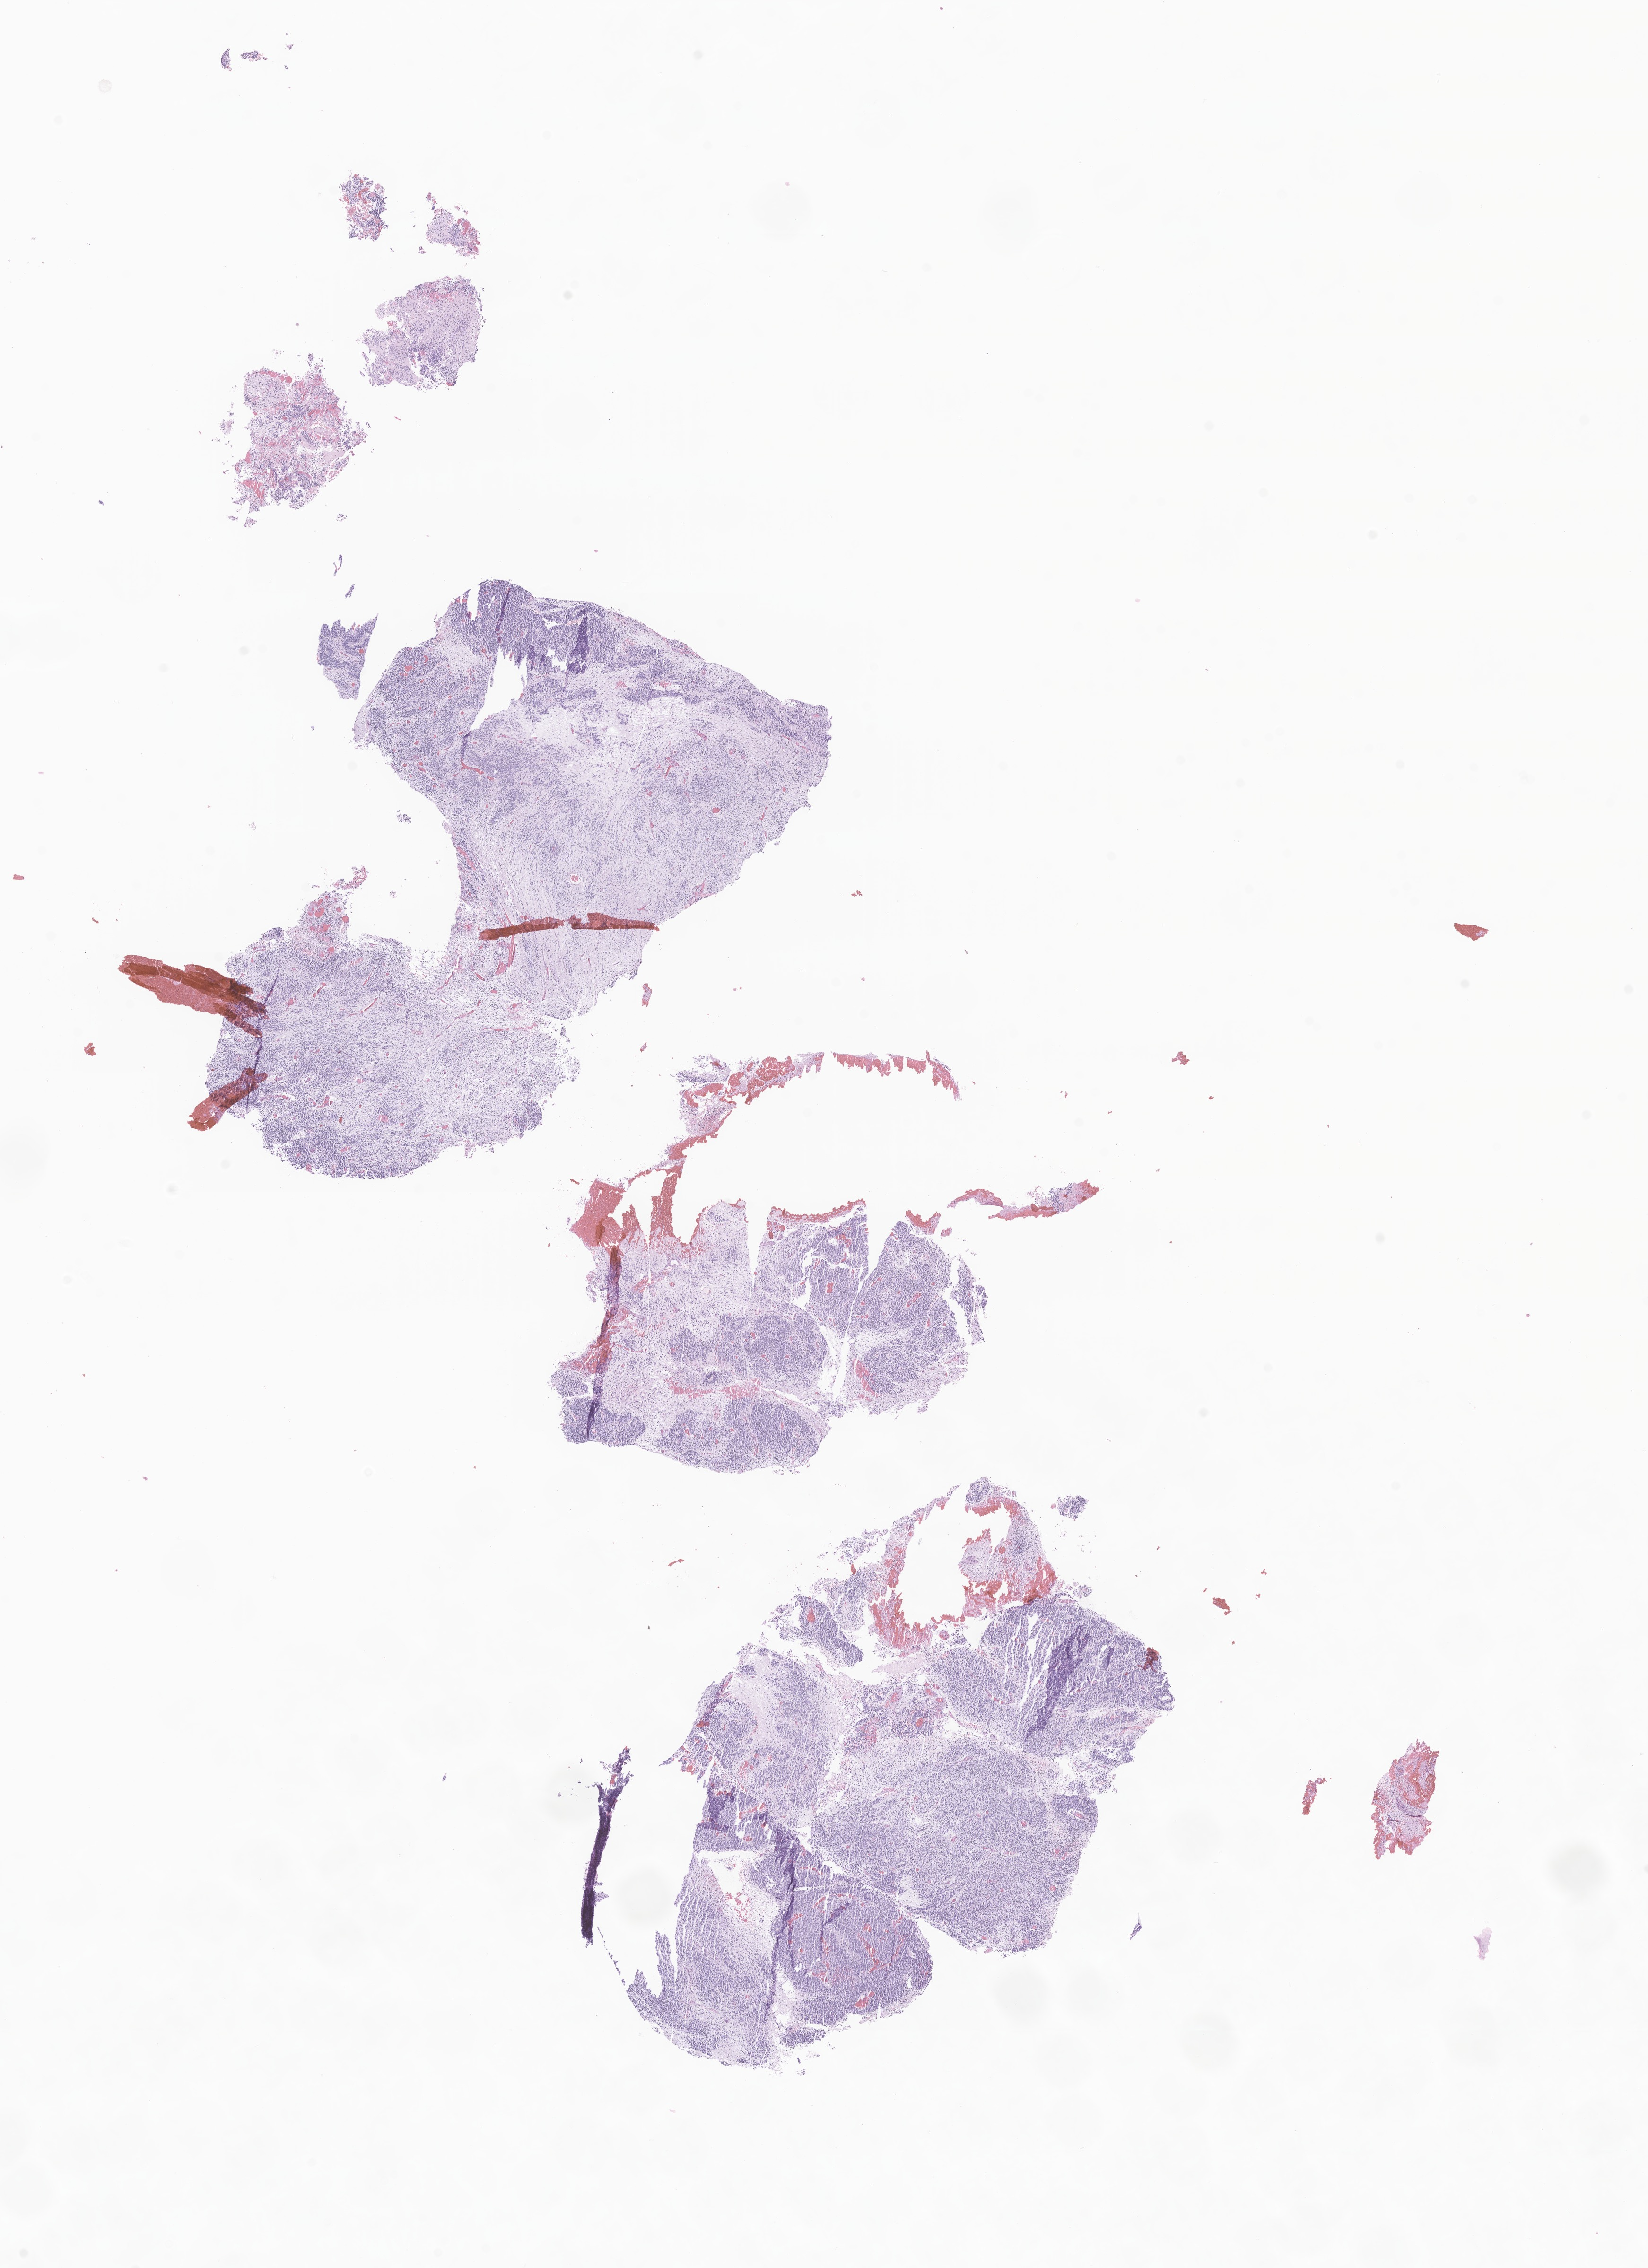
Digitized hematoxylin and eosin (H&E)-stained section of tumor tissue from the brain — low-resolution overview of the scanned area, about 14.7 x 20.2 mm, formalin-fixed paraffin-embedded section. Patient female; age 616 days (about 1.7 years).
Diagnosis (ICD-O-3 morphology term): Neoplasm, malignant.